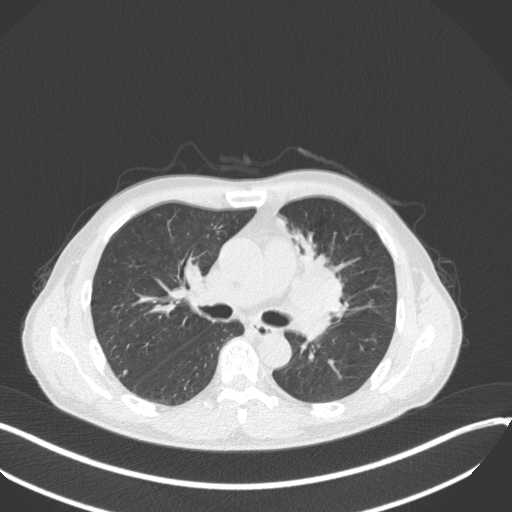
Chest CT, one axial slice. Position 201 of 411 along the scan axis. Reconstruction kernel B31f. 120 kVp. Lung window (W 1500 / L -600 HU). 512 × 512 image matrix, field of view 400 × 400 mm. Male patient, age 56 years. From the clinical record (not read from this slice): clinical TNM (as recorded): T2a N0 M0.
Annotated regions visible in this slice (rectangle marked by the reading radiologist):
- lung tumour (recorded histology: squamous cell carcinoma): box from (x=290, y=232) to (x=354, y=318) px